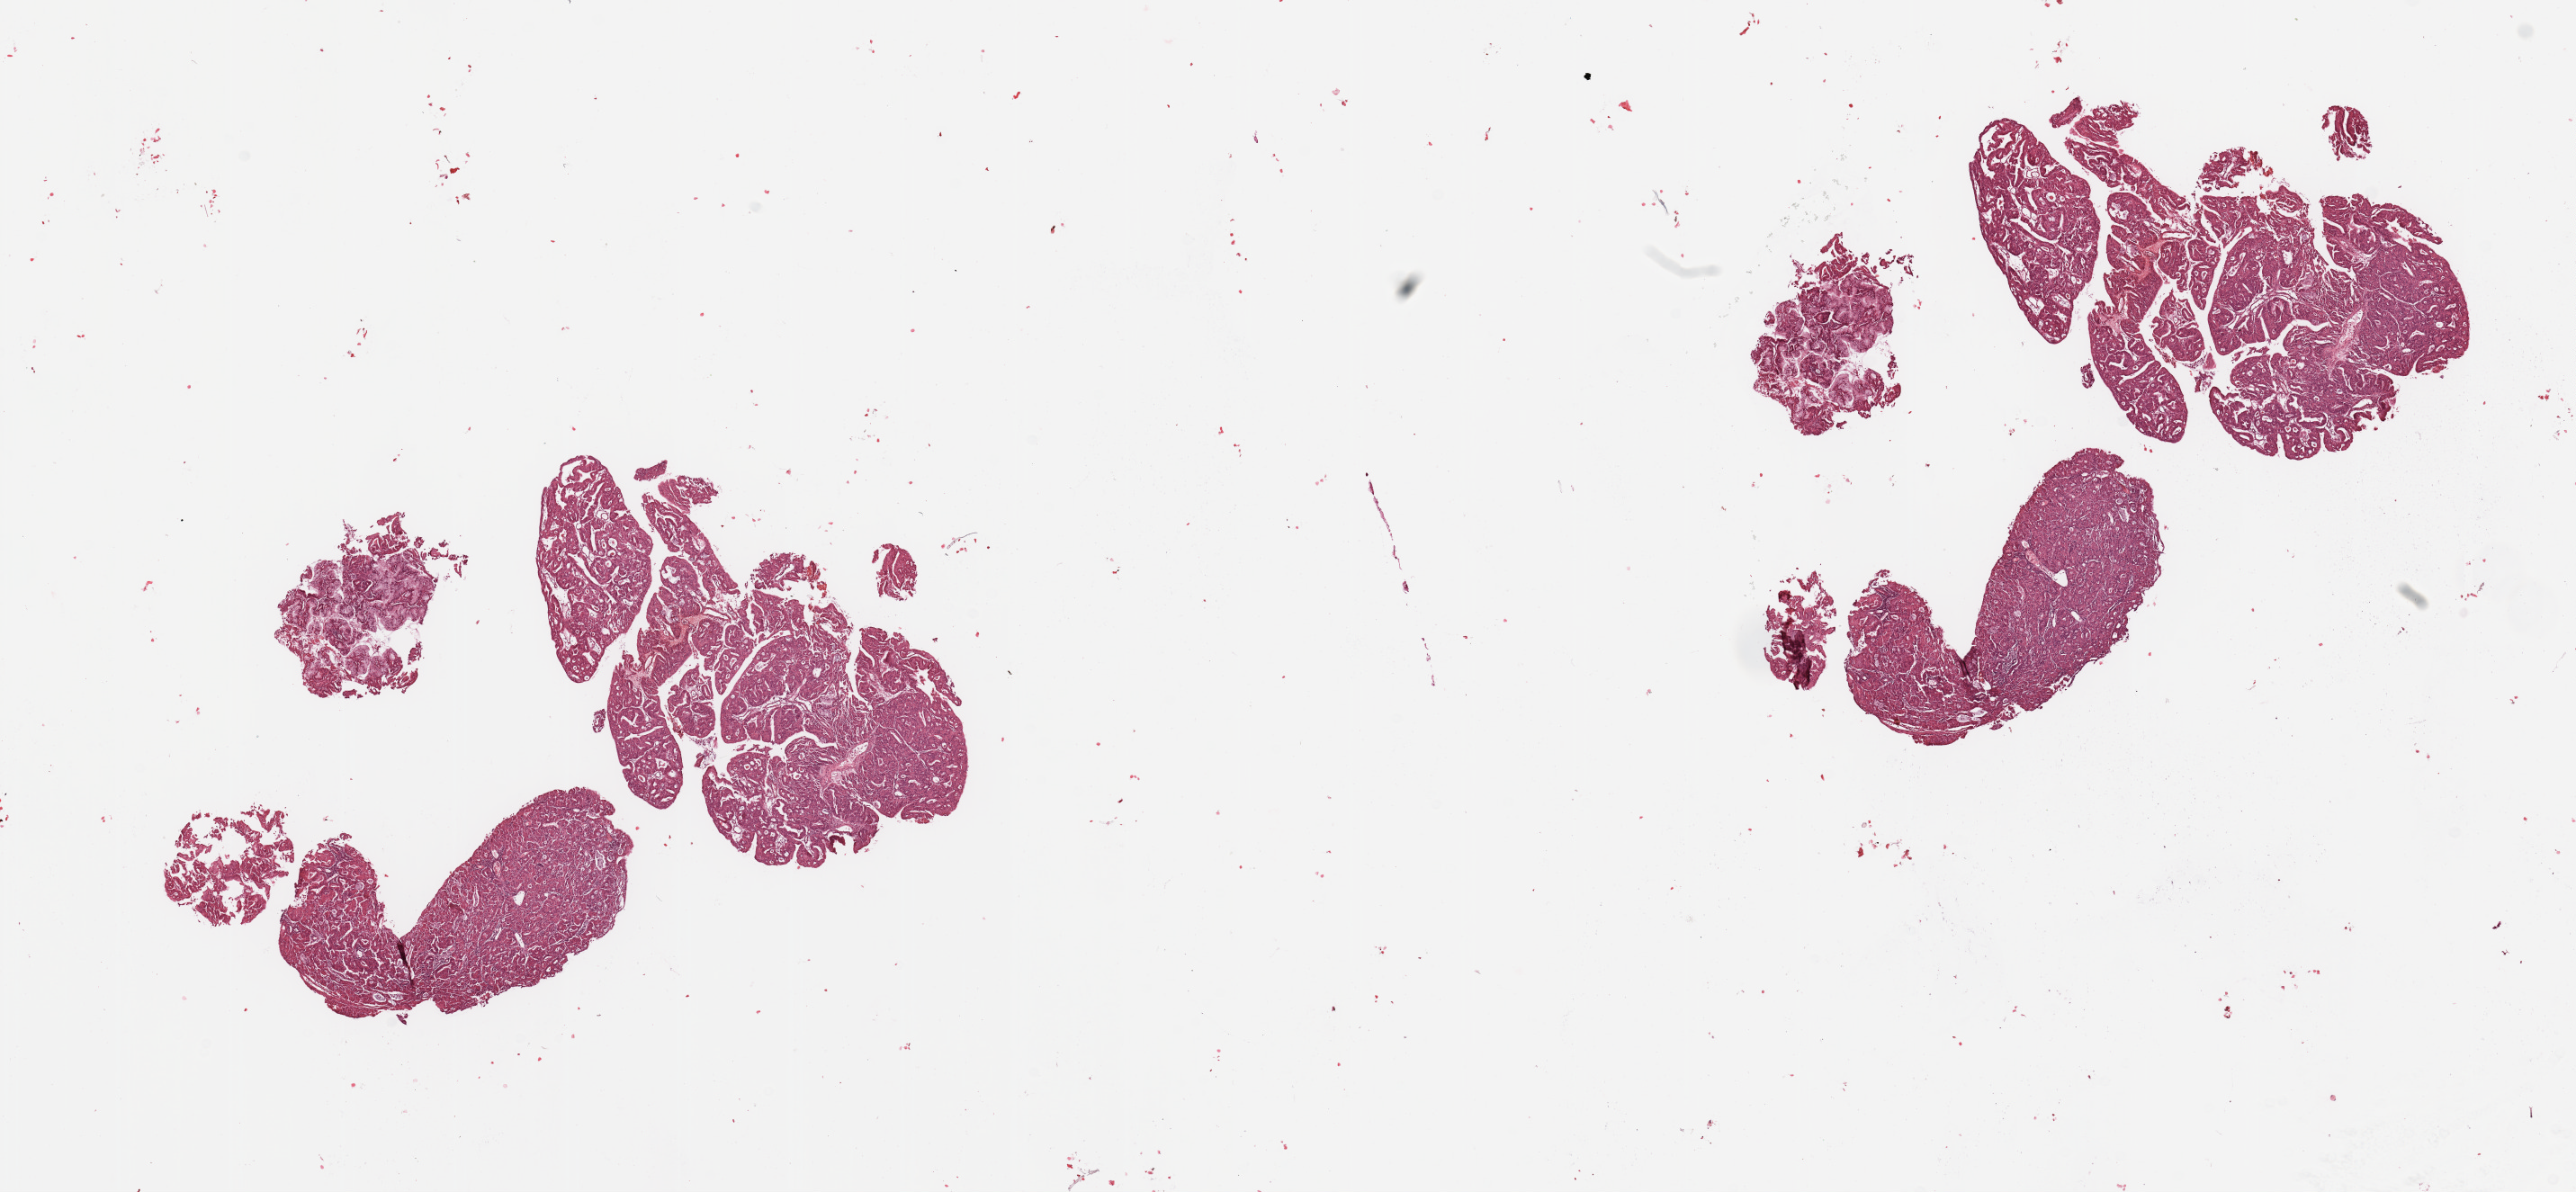
Whole-slide histology image, Hematoxylin and eosin (H&E) stained — low-resolution overview of the scanned area, about 22.6 x 10.5 mm (slide scanned at 20x); tumour tissue sample, sampled site: uterus. 61-year-old female patient. Histologic grade: G2 (moderately differentiated). Composition of this section per pathologist review: tumour nuclei 90%, necrosis 2%.
* primary tumour site (as recorded): anterior endometrium
* AJCC pathologic stage: I
* histologic diagnosis: Endometrioid adenocarcinoma, NOS